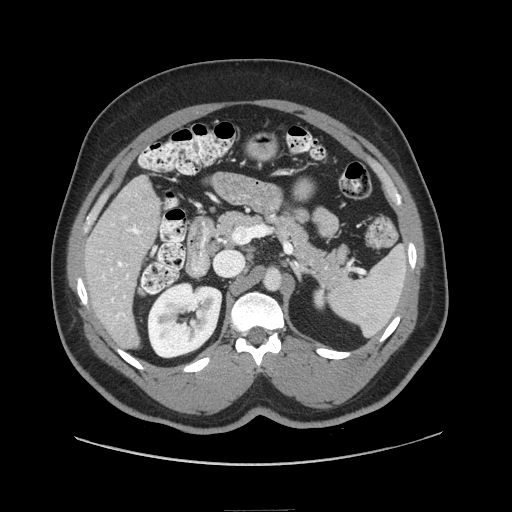
Contrast-enhanced abdominal CT (liver protocol), one axial slice; position 35 of 87 along the scan axis; reconstruction kernel STANDARD; 140 kVp; soft-tissue window (W 400 / L 40 HU); 2.5 mm slice thickness; 512 × 512 image matrix, field of view 440 × 440 mm. Case-level facts recorded for this patient, not image findings: diagnosis: hepatocellular carcinoma (patient treated with transarterial chemoembolisation; whether this scan precedes or follows treatment is not stated here); TNM stage (as recorded): Stage-II; Child-Pugh class: A.
Structures marked on this image (semi-automatic segmentation, software-assisted and operator-edited):
- liver parenchyma outside the tumour (the mass and vessels are separate outlines, so this box may not span the whole liver): bounding box <84,176,160,348> (left, top, right, bottom; pixels)
- liver vessels: <100,215,141,321>